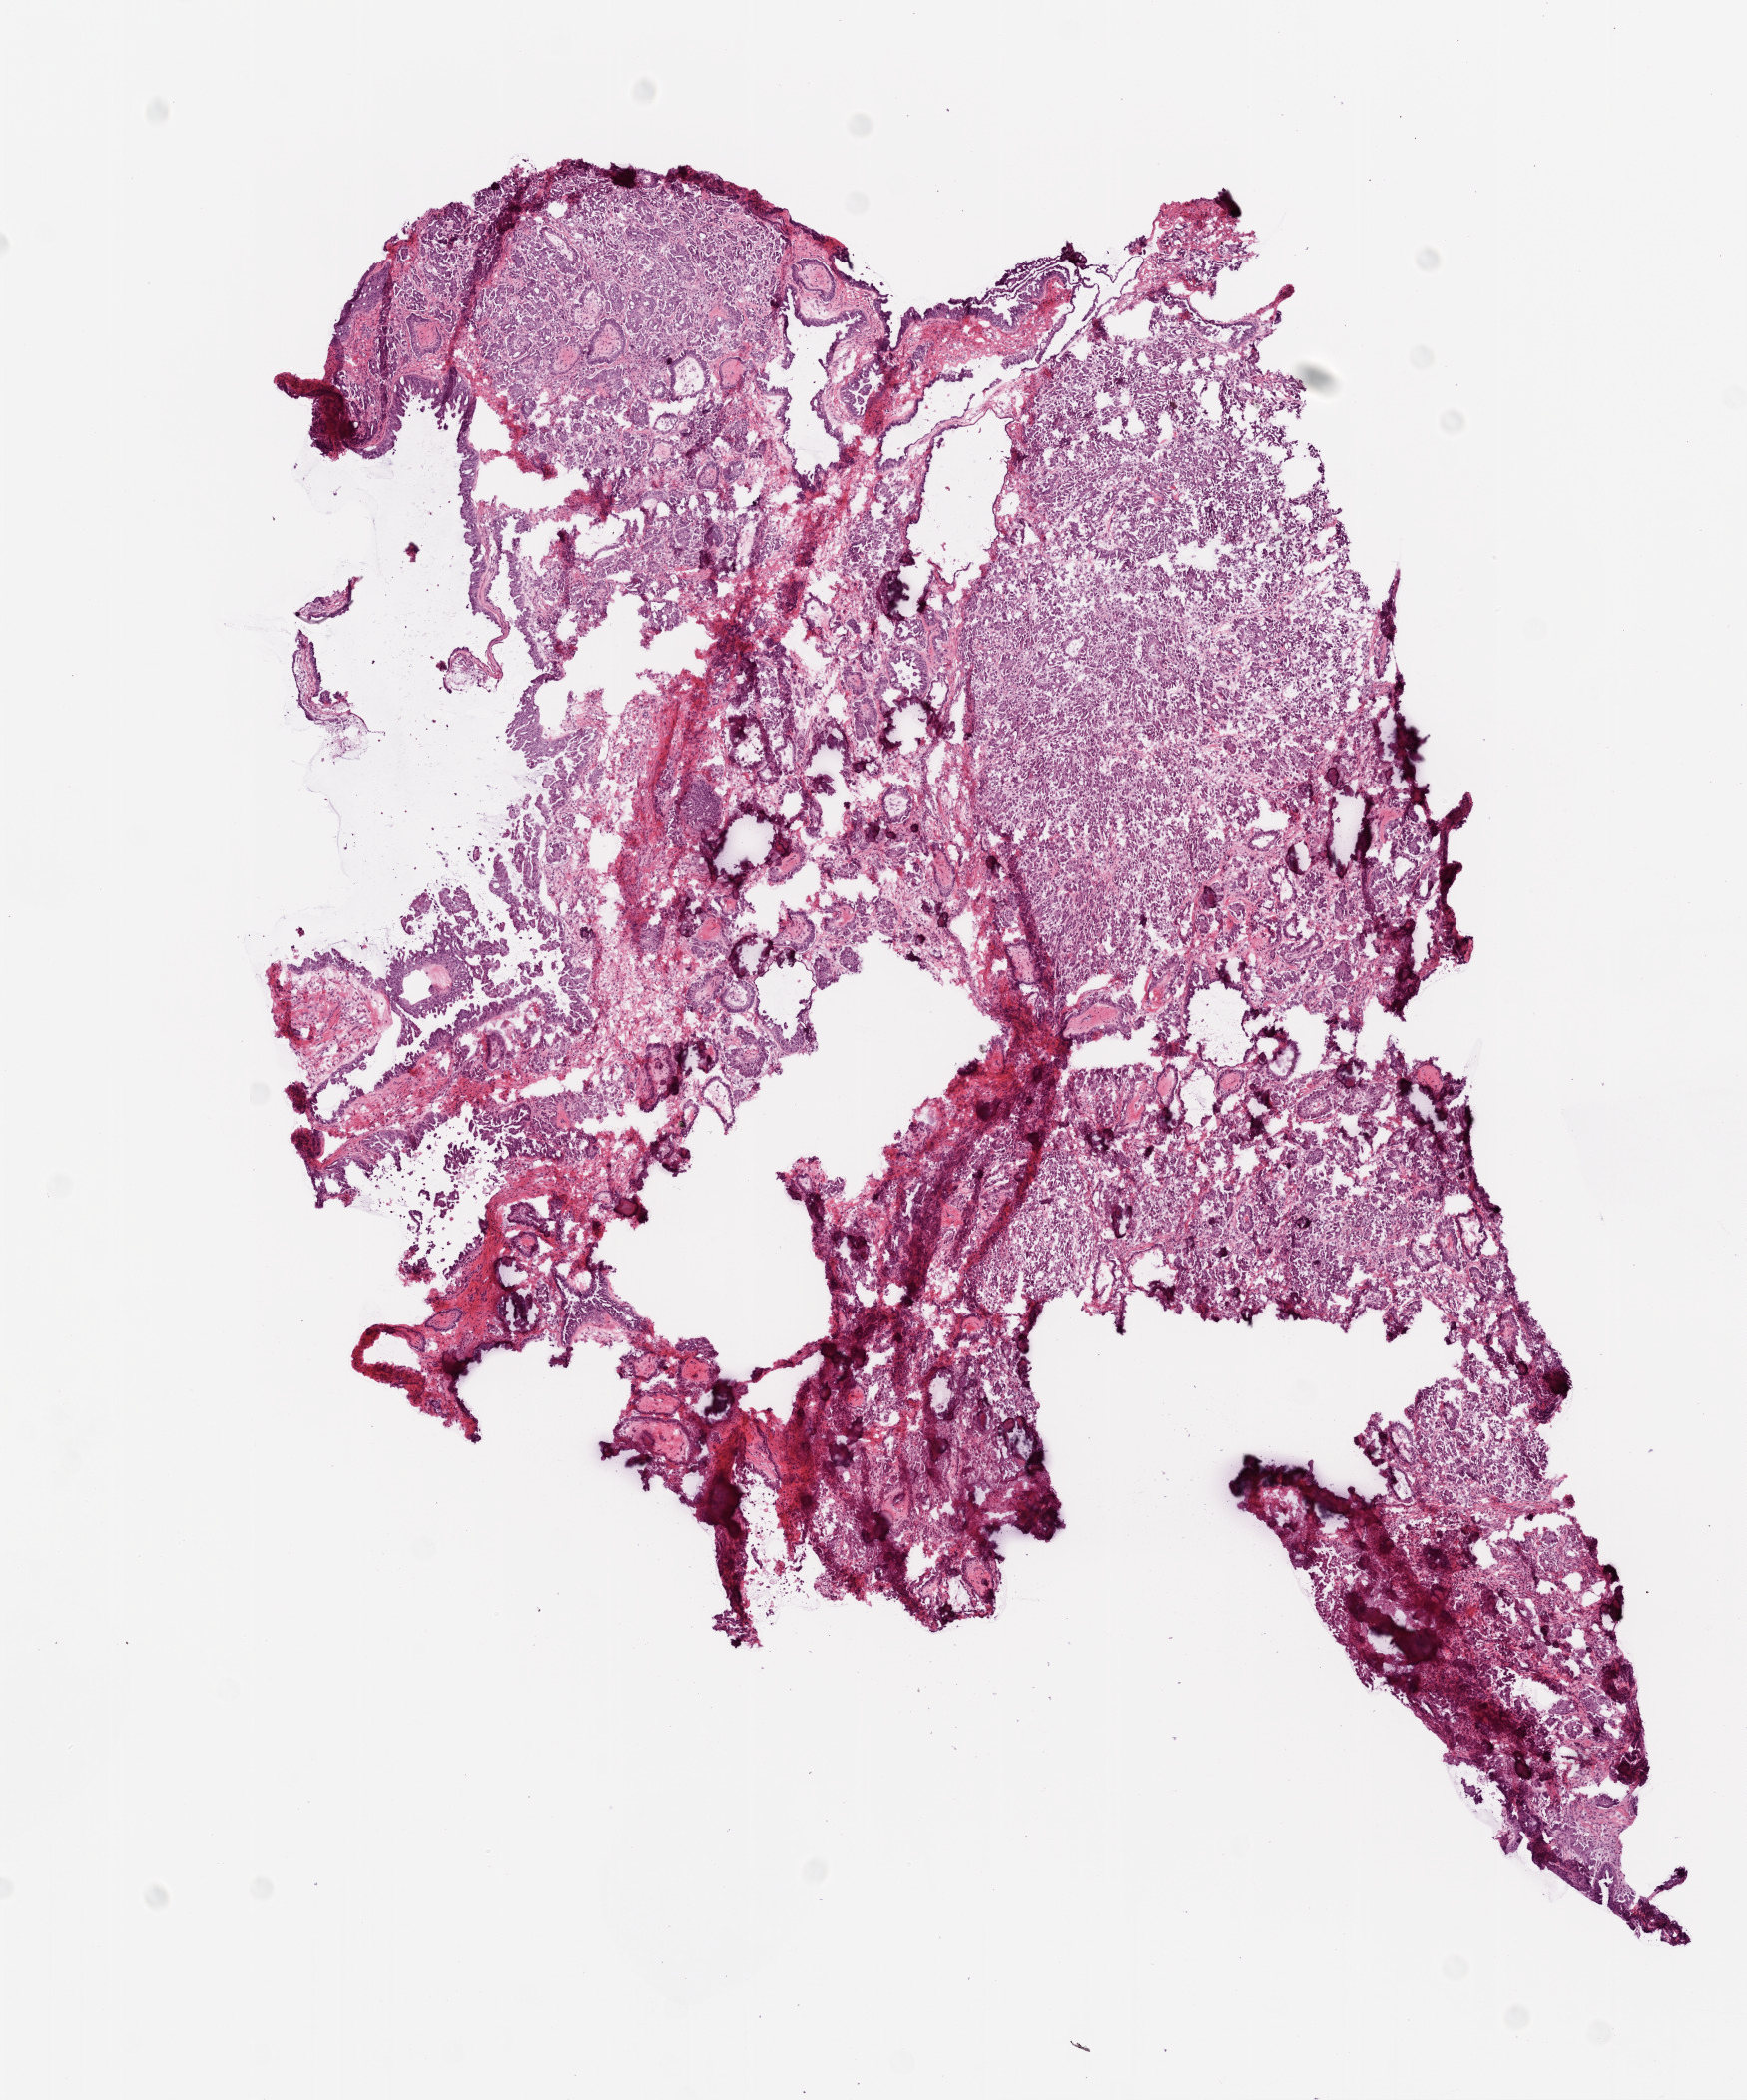
Whole-slide histology image, Hematoxylin and eosin (H&E) stained, shown as a low-resolution overview of the whole scanned area (about 7.0 x 8.4 mm), frozen section from the top of the tissue portion, sample: primary tumour, ovary. Patient: female, age at initial diagnosis 78 years. Histologic grade: G1 (well differentiated). Pathologist review of this section (percent, as recorded): tumour cells 85%, tumour nuclei 90%, normal cells 0%, stromal cells 15%, necrosis 0%.
* laterality: right
* FIGO stage: IIIC
* diagnosis: Serous cystadenocarcinoma, NOS